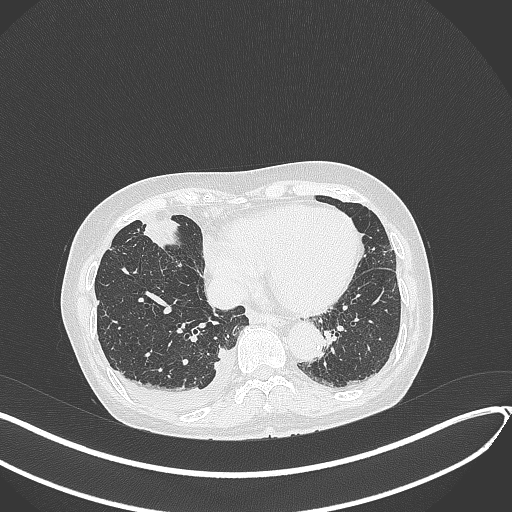
Chest CT, one axial slice. Slice 117 of 418 in the series (ordered by position). Reconstruction kernel B70f. 120 kVp. Lung window (W 1500 / L -600 HU). 1 mm slice thickness. 512 × 512 image matrix, field of view 400 × 400 mm. Patient: female, 75 years. From the clinical record (not read from this slice): clinical TNM (as recorded): T2a N3 M0.
Annotated regions visible in this slice (rectangle marked by the reading radiologist):
- lung tumour (recorded histology: adenocarcinoma): bounding box <131,209,186,251> (left, top, right, bottom; pixels)